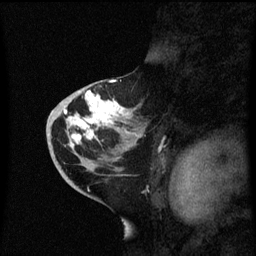
Breast MRI (dynamic contrast-enhanced), one sagittal slice; slice 34 of 60 in the series (ordered by position); dynamic contrast-enhanced series, image 2 of 3 at this slice position (ordered by acquisition); 1.5 T; TE 4.2 ms, TR 8.4 ms; 2.3 mm slice thickness; 256 × 256 image matrix, field of view 200 × 200 mm. Patient: female, 46 years. From the clinical record (not read from this slice): setting: breast cancer imaged before/during neoadjuvant chemotherapy; receptor status: HER2-positive.
Annotated regions visible in this slice (semi-automatic segmentation, software-assisted and operator-edited):
- analysis volume of interest (the breast-tissue region the enhancement analysis was run in; not a lesion): bounding box [x1, y1, x2, y2] px = [46, 86, 145, 171]
- tumour enhancement mask (voxels above the 70 % enhancement threshold inside the analysis volume of interest): [66, 92, 129, 147]